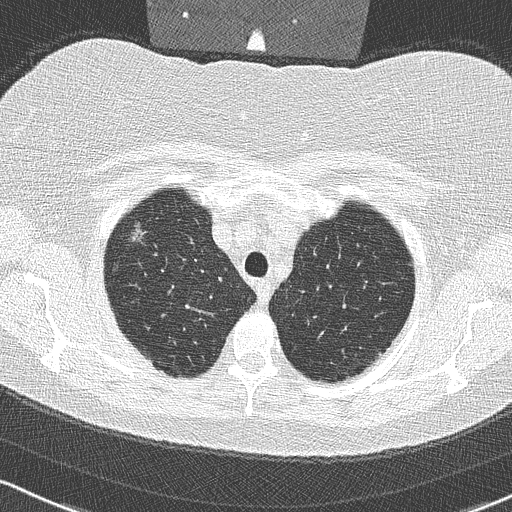
Low-dose screening chest CT, axial slice. Third screening round (two years after baseline). Lung window (W 1500 / L -600 HU). 2 mm slice thickness. Lung (sharp) reconstruction kernel (B50f). Slice 49 of 315 in the series. 512 × 512 image matrix. Female participant, aged 58 years at enrolment.
Lesion marked by an expert reader, bounding box [x1, y1, x2, y2] px = [121, 217, 161, 252]. The screening reader recorded 2 non-calcified nodules or masses ≥4 mm on this exam; which of them this box marks is not recorded. Official screen result: positive, other. Lung cancer was diagnosed 48 days after this screen: bronchiolo-alveolar adenocarcinoma, NOS, right upper lobe, well differentiated (G1), stage IA (AJCC 6th edition), 9 mm at pathology.